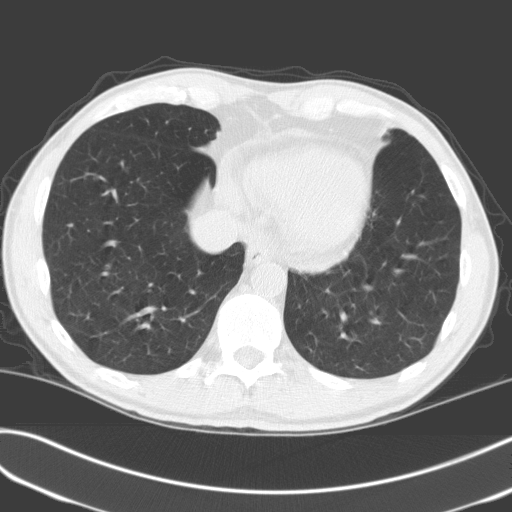
Low-dose screening chest CT, one axial slice; slice 49 of 170 in the series (ordered by position); 120 kVp; lung window (W 1500 / L -600 HU); 3.2 mm slice thickness; 512 × 512 image matrix.
Outlined on this slice (outlined manually by an expert reader):
- lesion 1 (tumor, upper lobe of left lung): bounding box [x1, y1, x2, y2] px = [375, 121, 391, 137]